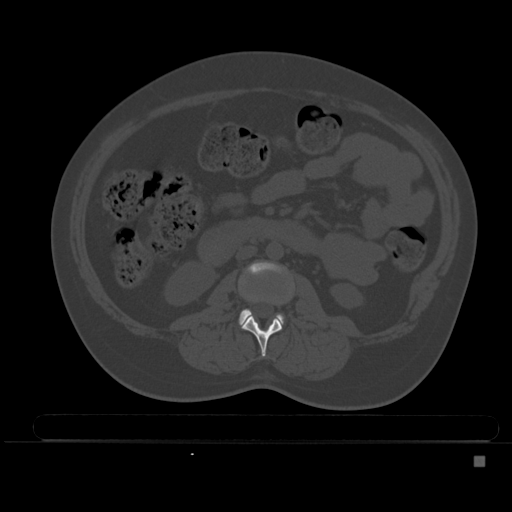
CT including the spine, one axial slice. Slice 163 of 495 in the series (ordered by position). Bone window (W 1800 / L 400 HU). 1.5 mm slice thickness. 512 × 512 image matrix, field of view 404 × 404 mm. Patient: female, 33 years. From the clinical record (not read from this slice): primary cancer: breast; vertebrae with lytic lesions (as recorded): T1.
Outlined on this slice (semi-automatic segmentation, software-assisted and operator-edited):
- L2 vertebra: bounding box (x1, y1, x2, y2) in pixels: (240, 314, 282, 357)
- L3 vertebra: (239, 262, 284, 325)